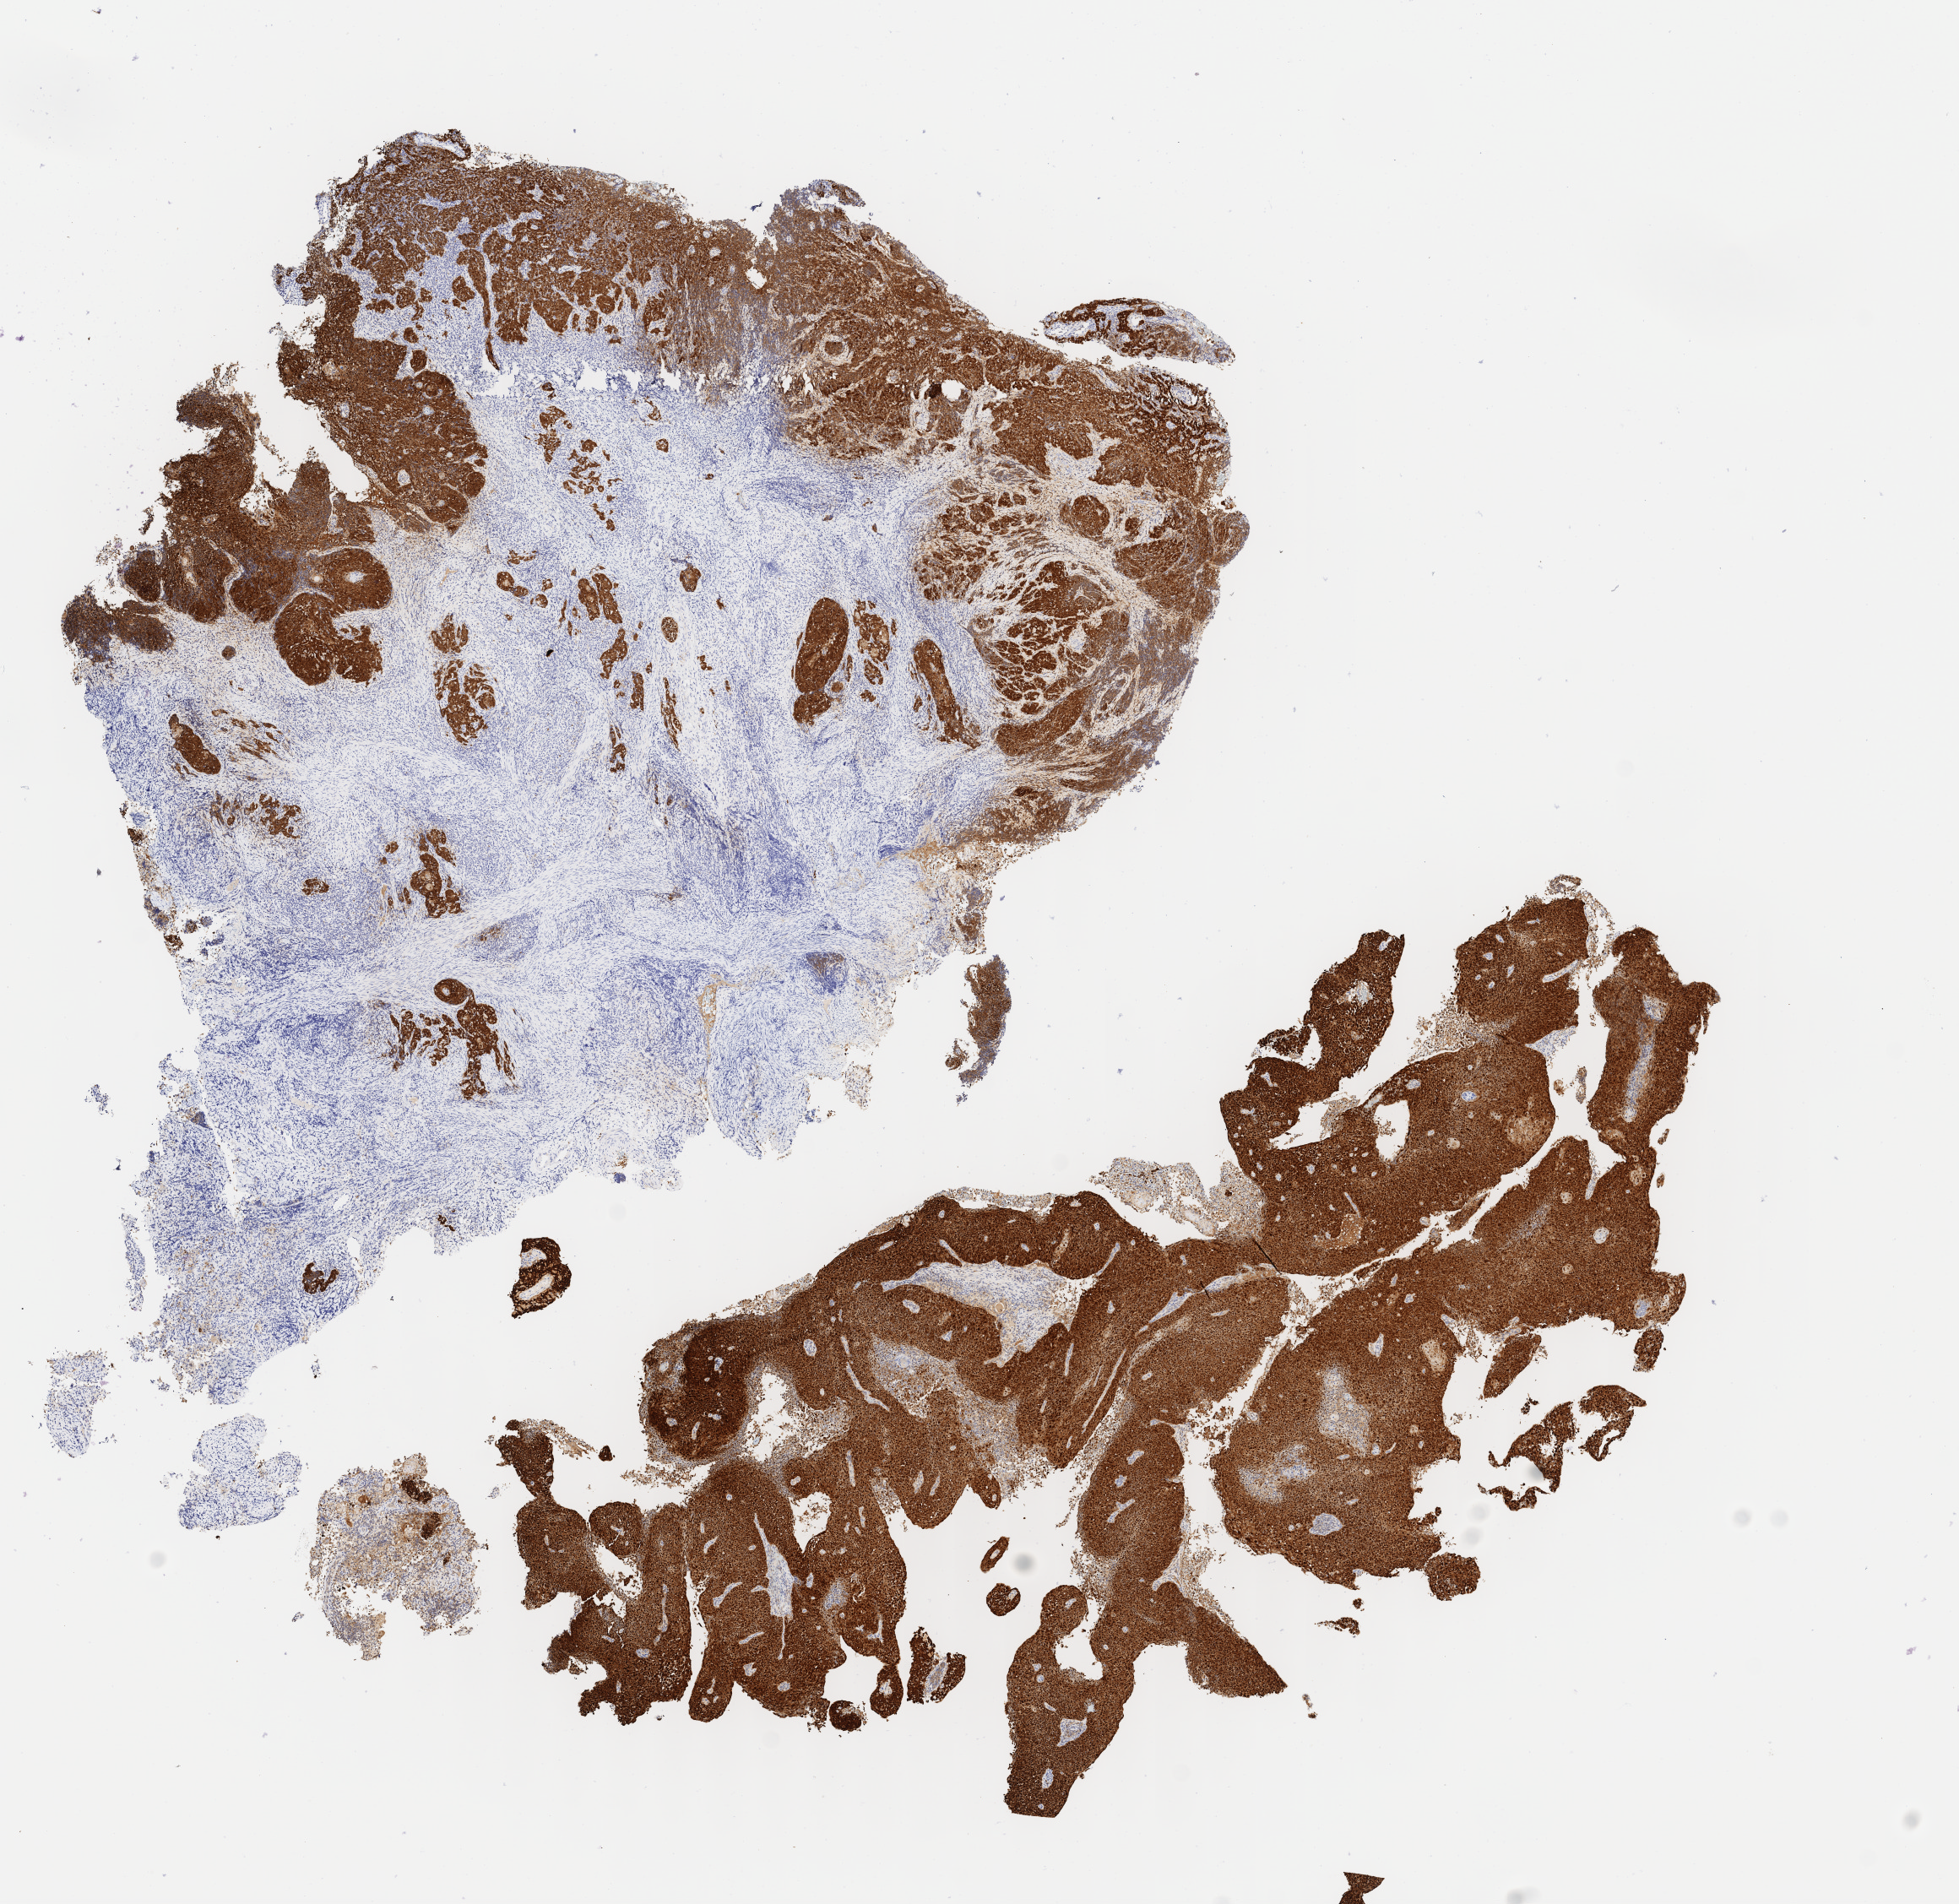
Whole-slide image, immunohistochemical stain for p16 (p16INK4a) — whole scanned area (about 9.2 x 9.0 mm) shown as a low-resolution overview; tumor tissue; site: cervix. Patient female; age 49 years.
- diagnosis: Squamous cell carcinoma, keratinizing, NOS